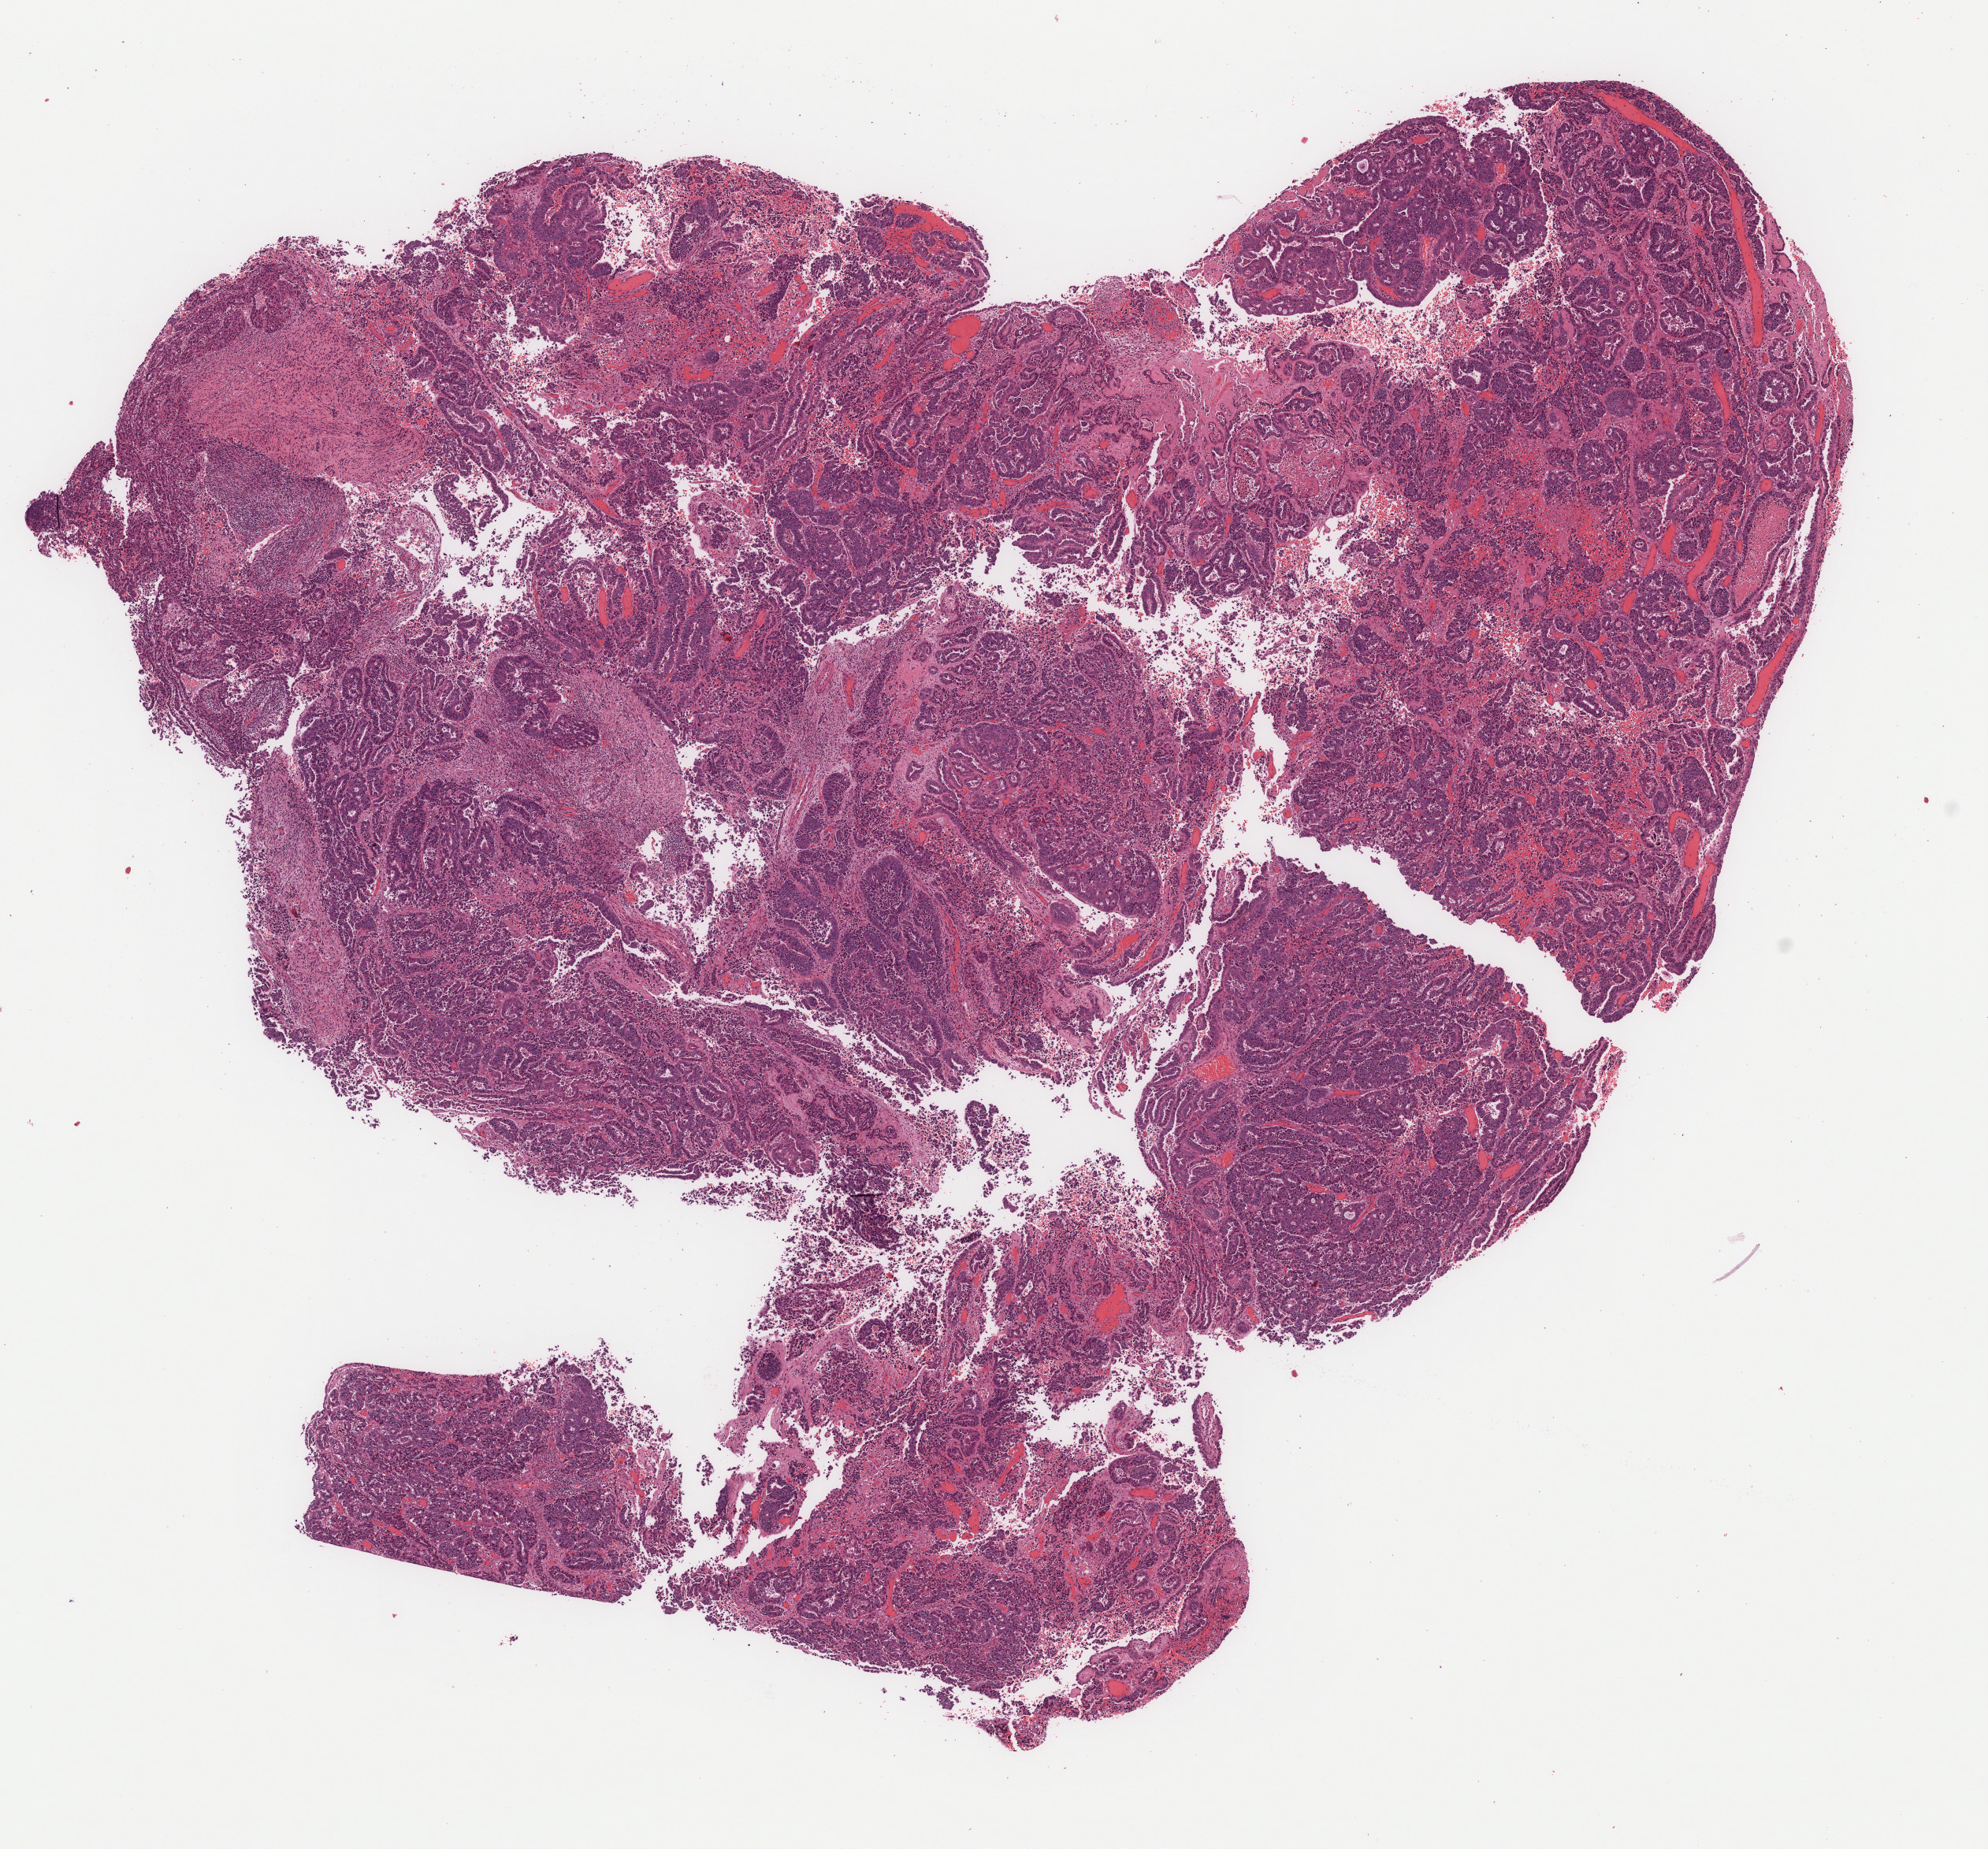
Digitized Hematoxylin and eosin (H&E) stained tissue section (whole slide), a low-resolution overview of the entire scanned area, about 10.2 x 9.5 mm (from a 40x scan), FFPE section, sample: primary tumour, uterus. Female patient; age at initial diagnosis 63 years. Histologic grade: G3 (poorly differentiated).
Pathologic diagnosis: Serous cystadenocarcinoma, NOS (endometrium). FIGO stage: IB.